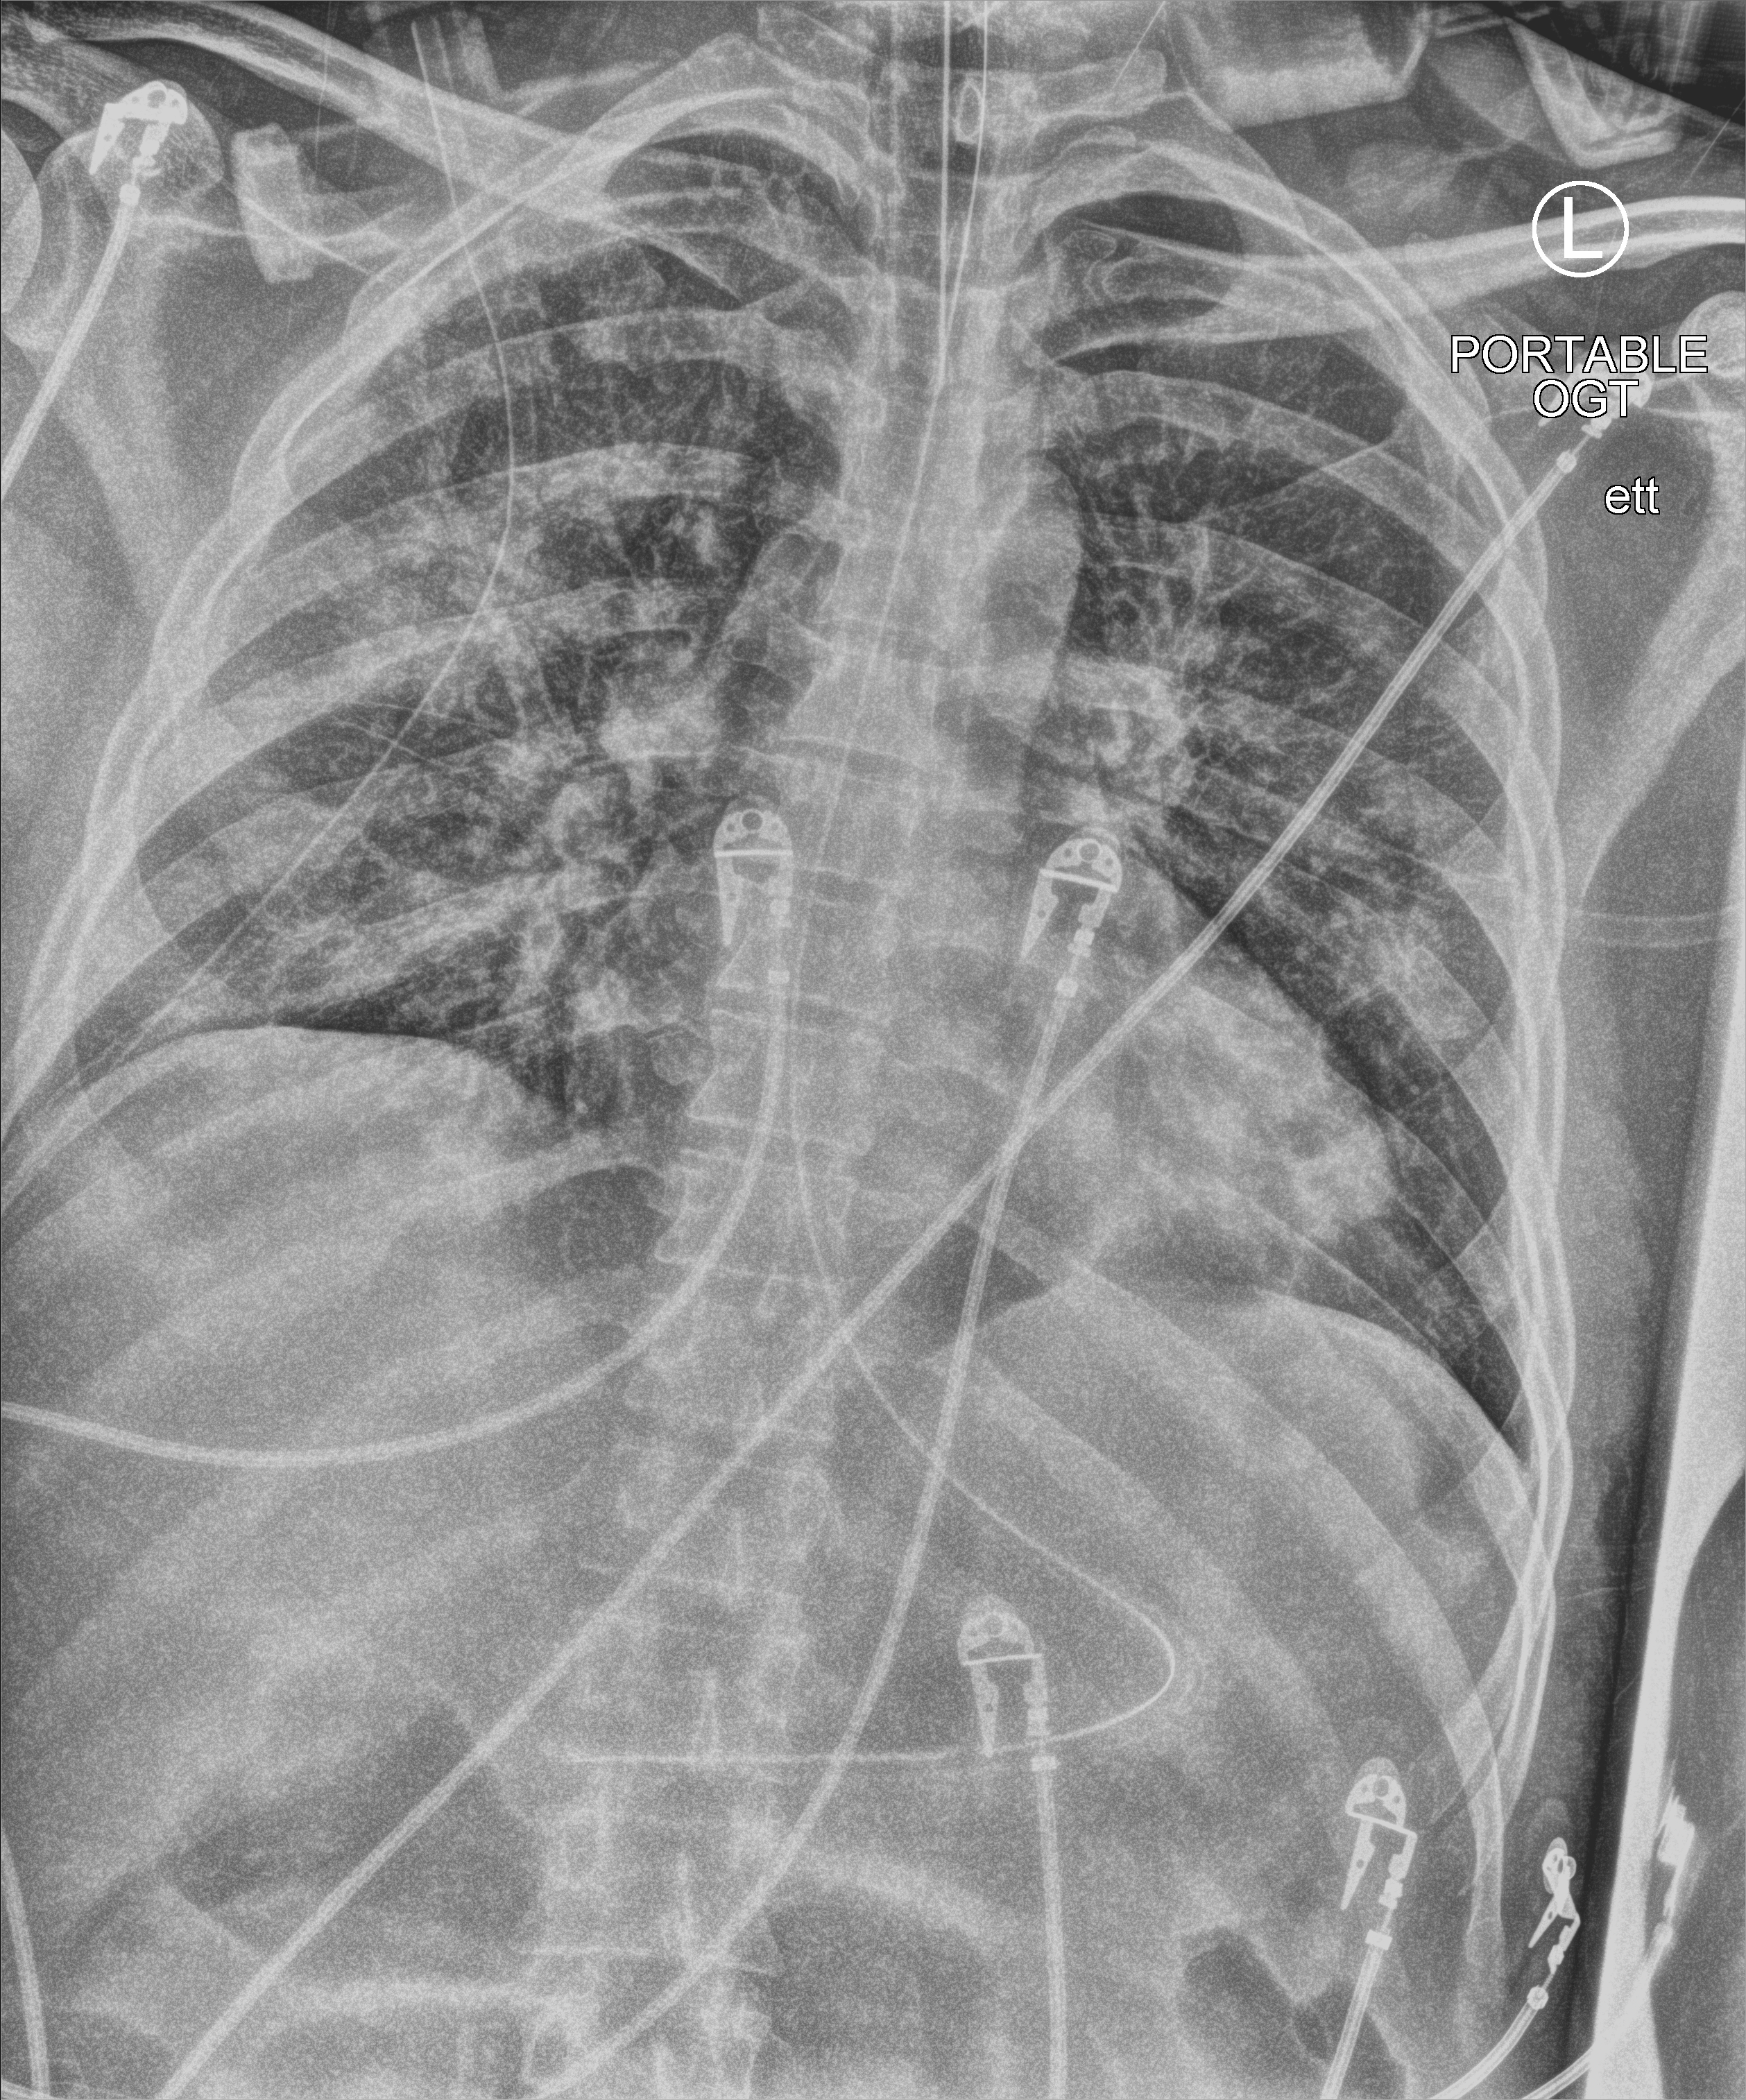
Portable chest radiograph. Patient hospitalised with COVID-19; male, aged 18–59 years.
From the hospital-stay record, not from the radiograph (when in the stay this image was taken is not recorded): admitted to intensive care during this hospital stay: yes; length of hospital stay: 31 days; mechanically ventilated during this hospital stay: yes.